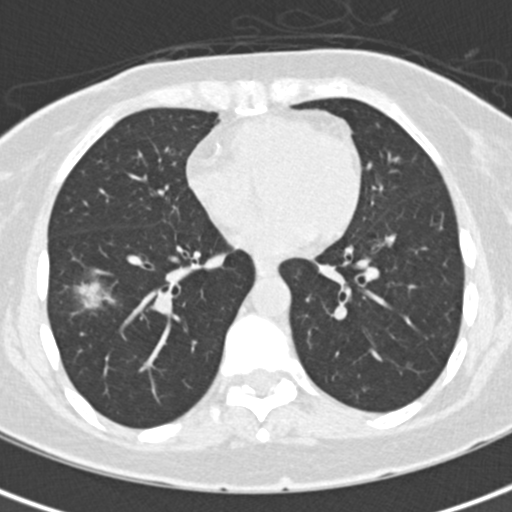
Low-dose screening chest CT, one axial slice. Position 72 of 171 along the scan axis. 120 kVp. Lung window (W 1500 / L -600 HU). 2 mm slice thickness. 512 × 512 image matrix, field of view 284 × 284 mm.
Outlined on this slice (outlined manually by an expert reader):
- lesion 1 (tumor, lower lobe of right lung): box from (x=72, y=282) to (x=115, y=315) px